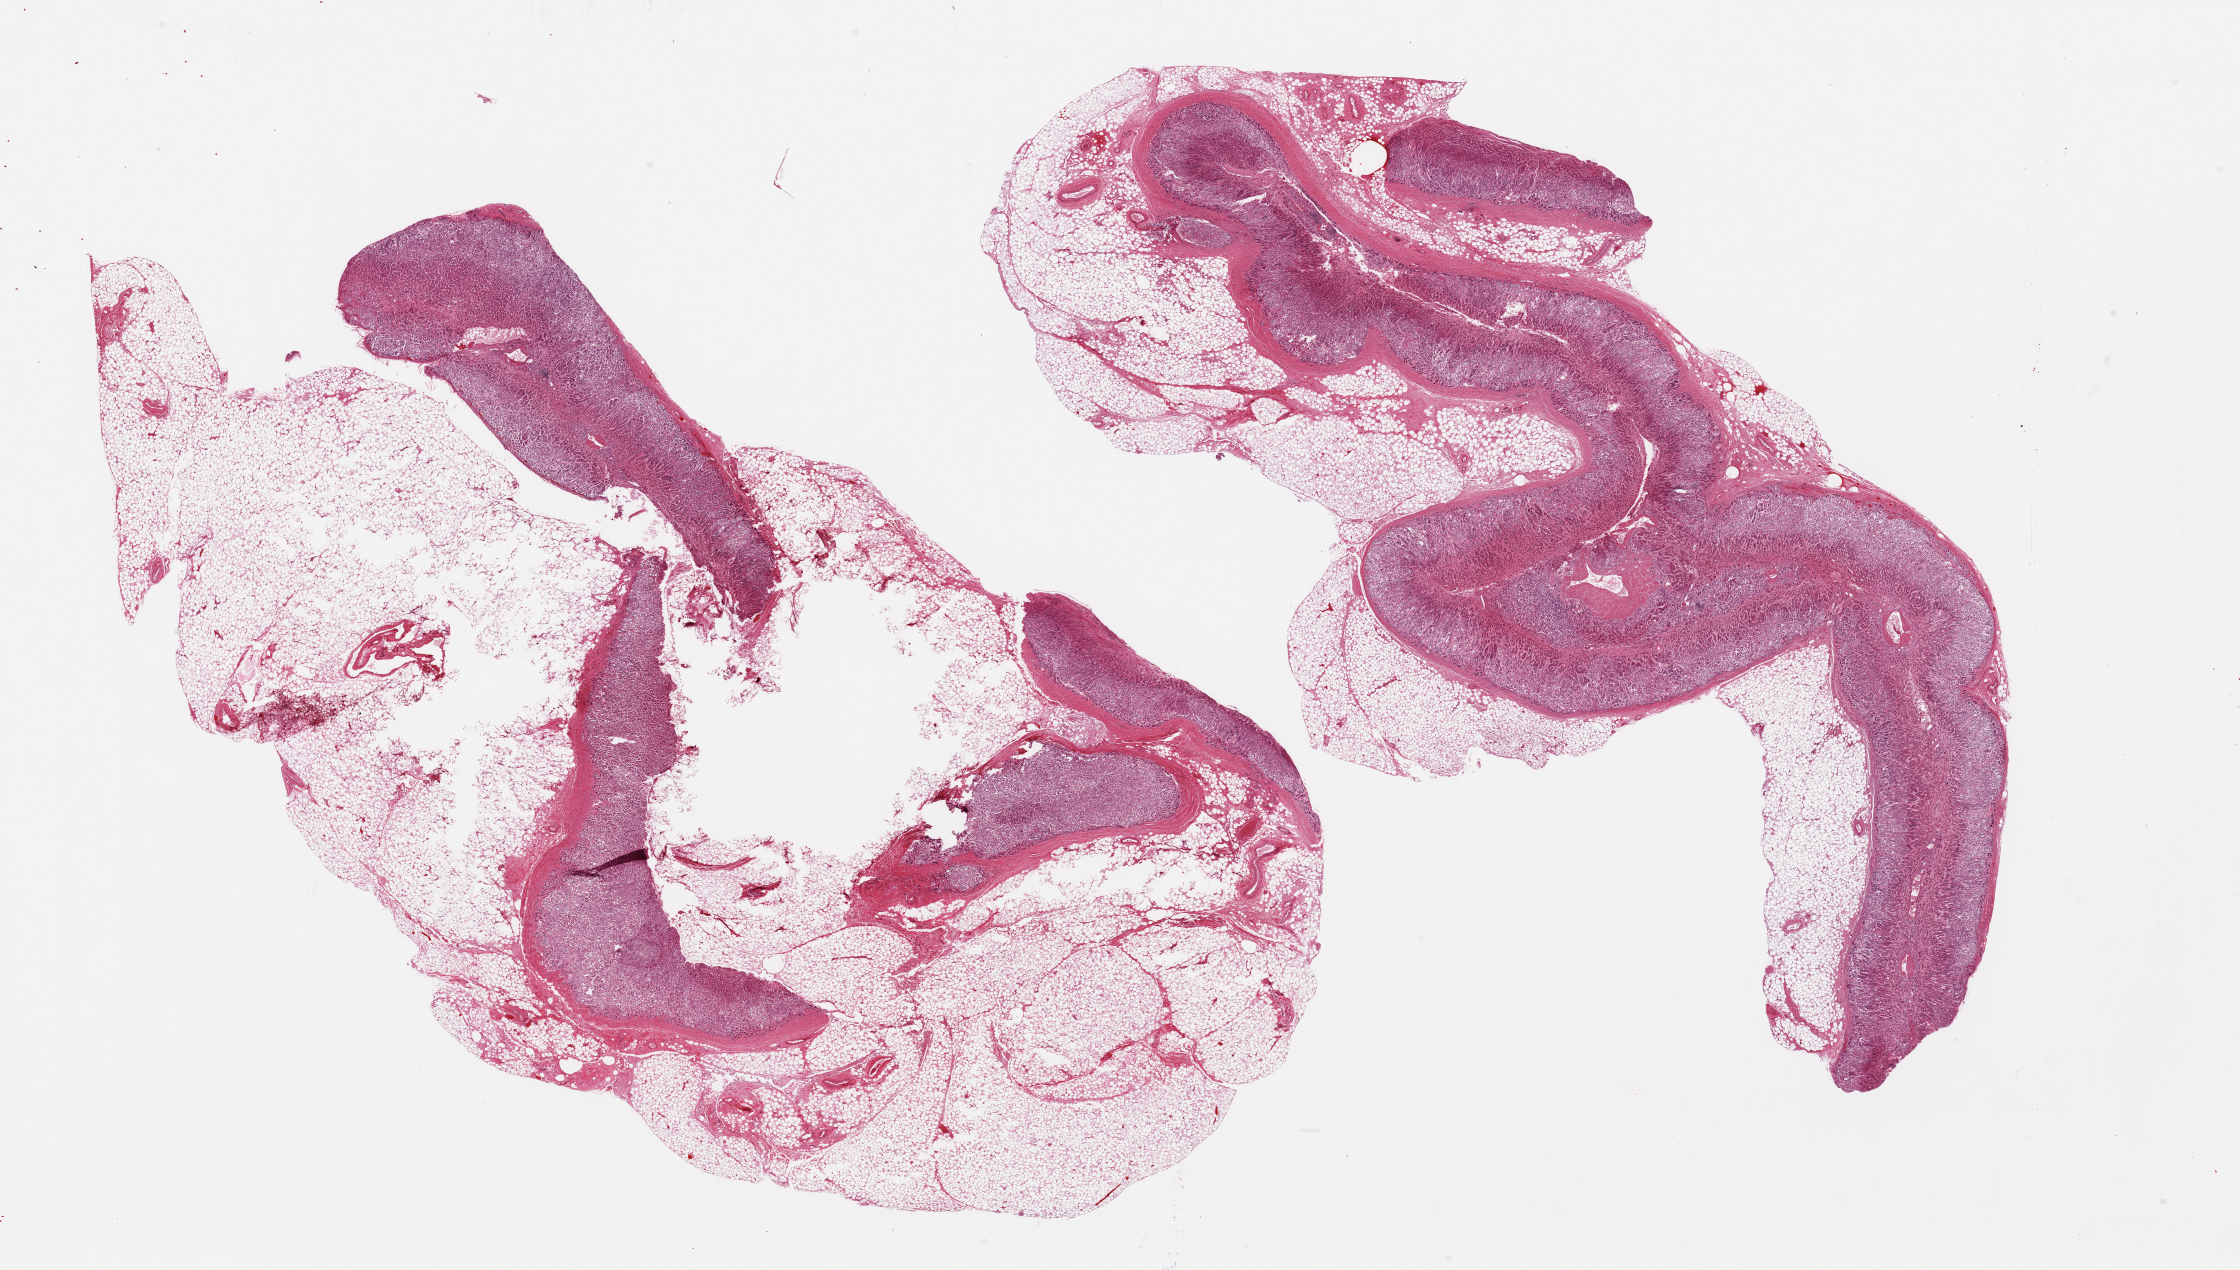
Whole-slide image, hematoxylin and eosin (H&E) stain — shown as a low-resolution overview of the whole scanned area (about 35.4 x 20.1 mm, from a 20x scan), PAXgene-fixed paraffin-embedded (PFPE) section, sampled site (target tissue): adrenal gland, donor tissue sample.
Pathologist's review note for this sample: 2 pieces, 19x9 & 19 x10 mm; 50 & 70% adipose tissue.